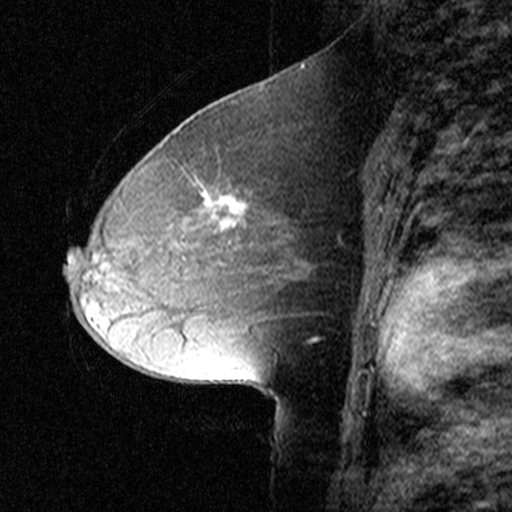
Breast MRI (dynamic contrast-enhanced), one sagittal slice; position 19 of 44 along the scan axis; dynamic contrast-enhanced study with each time point stored as its own series, time point 2 of 3 at this slice position (early post-contrast, ordered by acquisition time); 1.5 T; TE 4.5 ms, TR 11 ms; 3 mm slice thickness; 512 × 512 image matrix, field of view 200 × 200 mm. Female patient, age 50 years. From the clinical record (not read from this slice): setting: breast cancer imaged before/during neoadjuvant chemotherapy; receptor status: HR-positive, HER2-negative.
Structures marked on this image (semi-automatically segmented with operator editing):
- analysis volume of interest (the breast-tissue region the enhancement analysis was run in; not a lesion): bounding box <154,164,313,287> (left, top, right, bottom; pixels)
- tumour enhancement mask (voxels above the 90 % enhancement threshold inside the analysis volume of interest): <208,197,246,226>